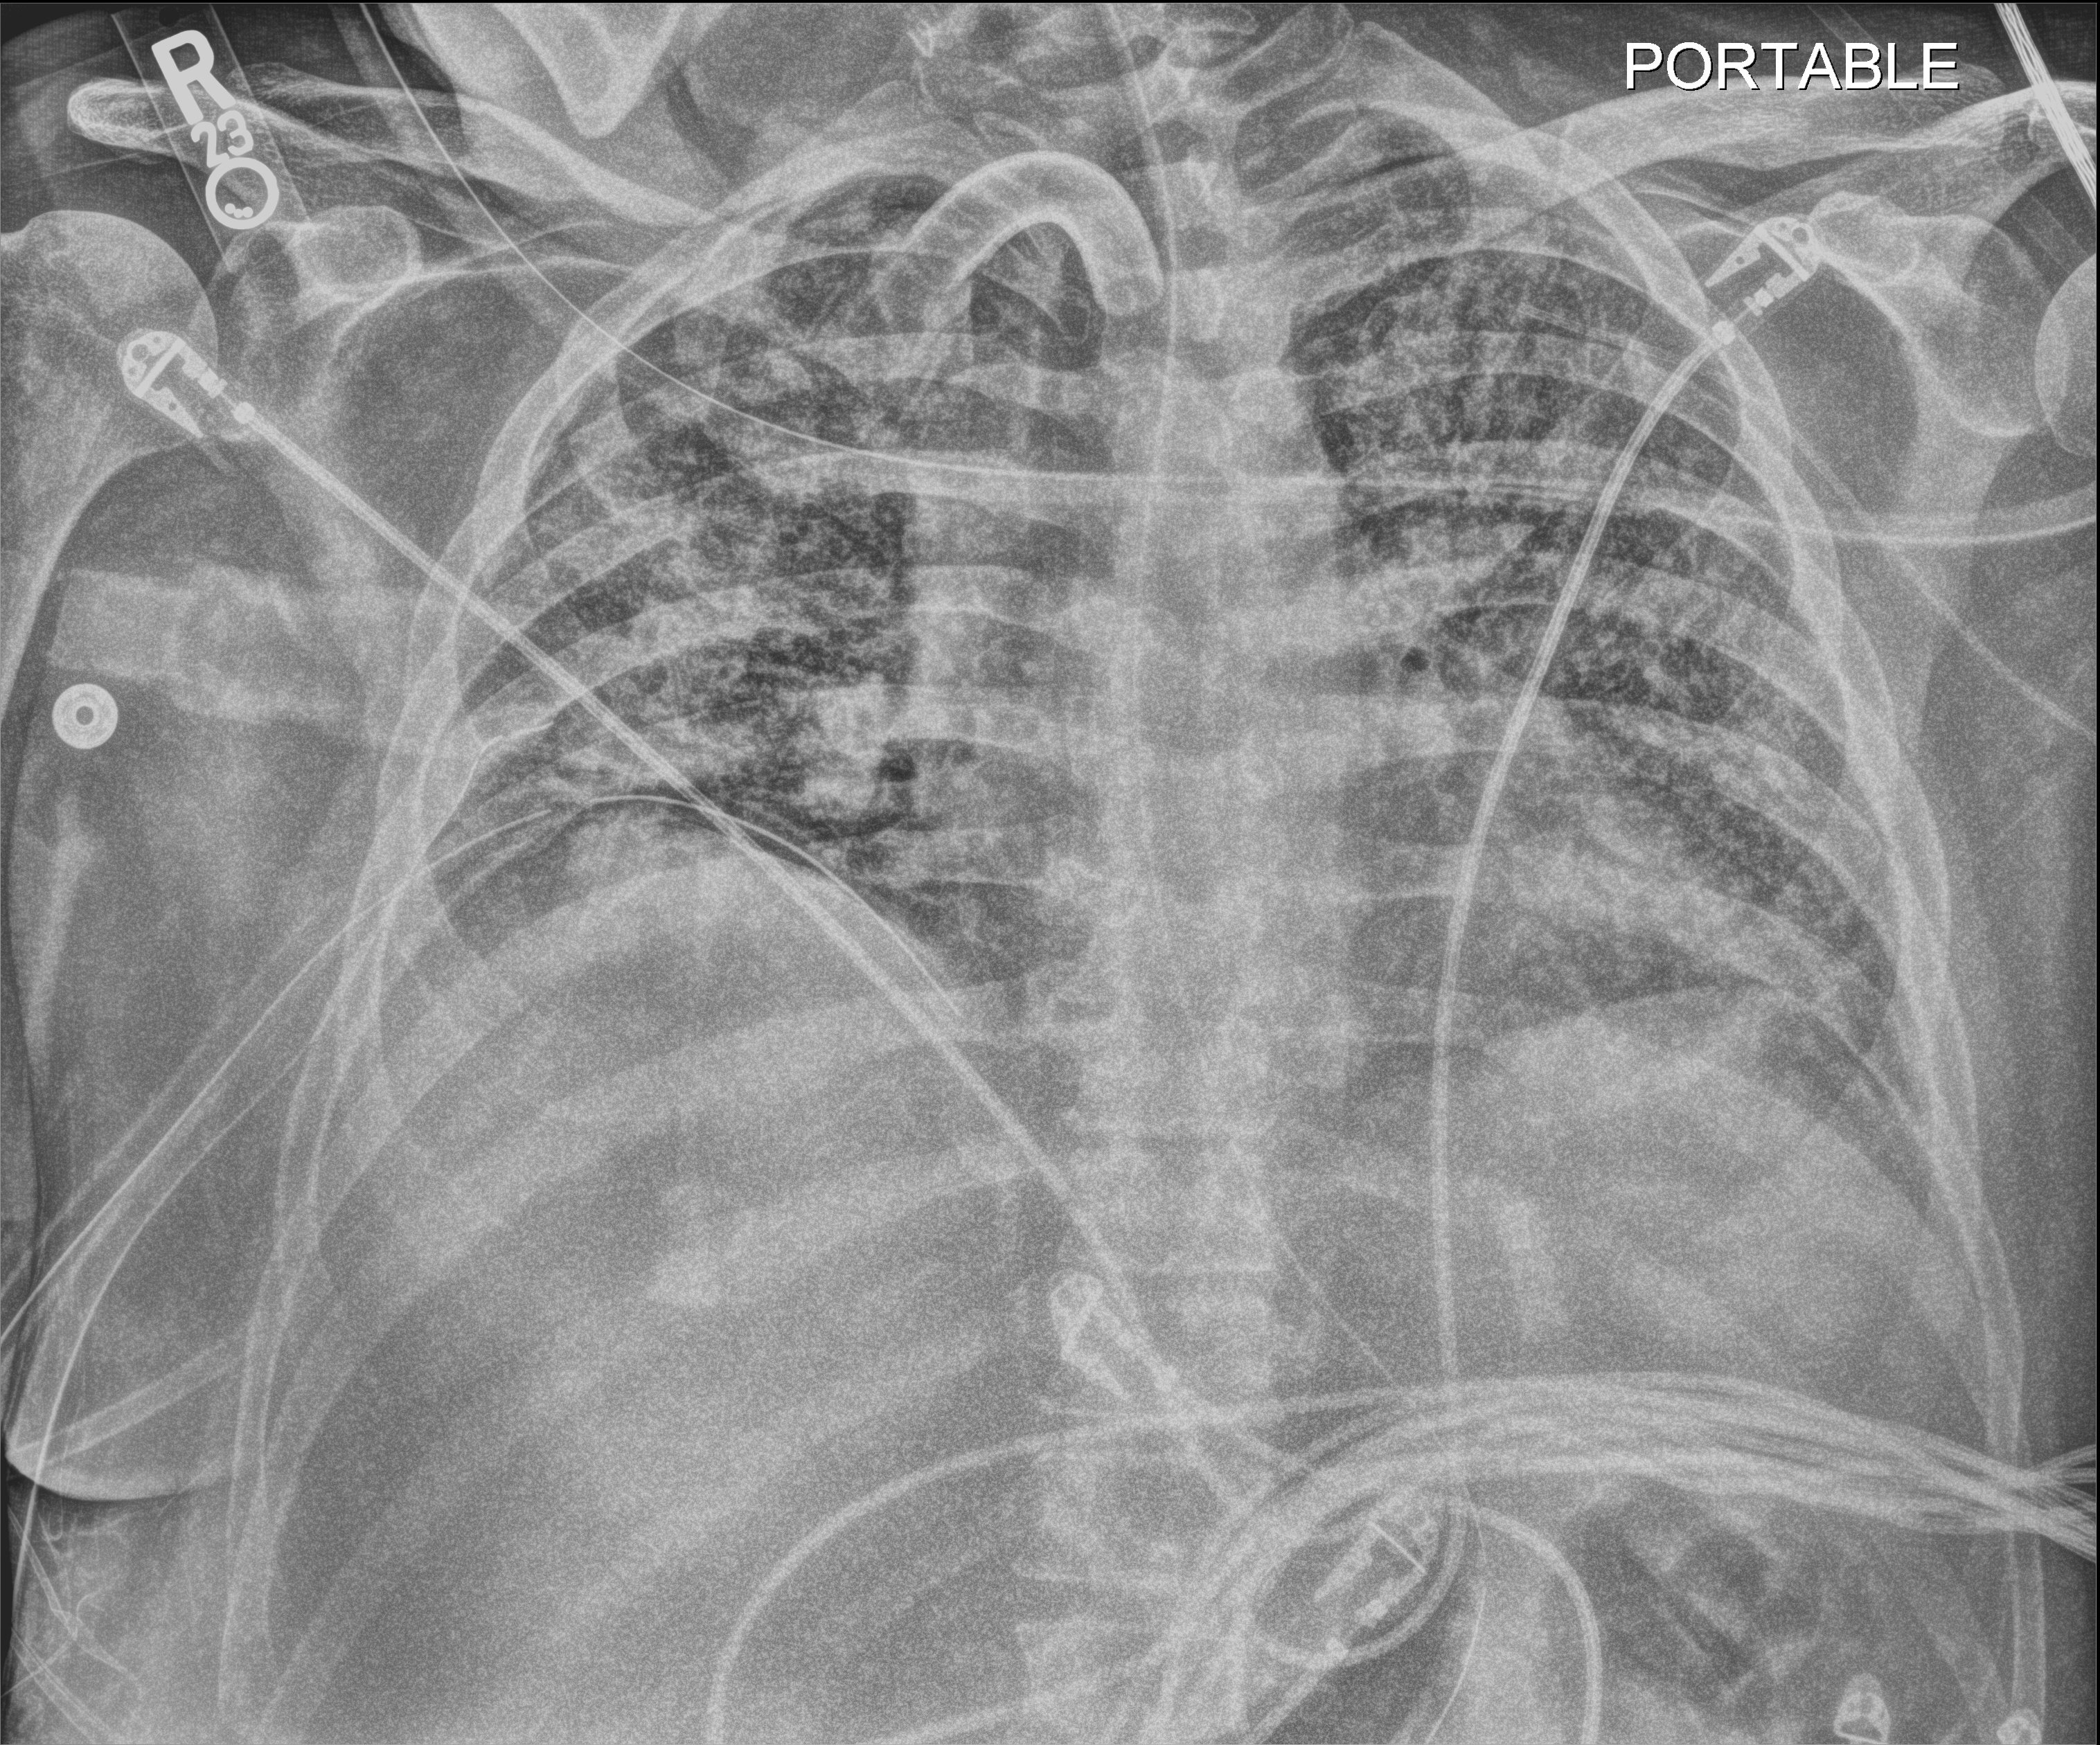
Portable chest radiograph; anteroposterior (AP) projection. Patient hospitalised with COVID-19; male, aged 18–59 years.
From the hospital-stay record, not from the radiograph (when in the stay this image was taken is not recorded): smoking status (admission record): never.